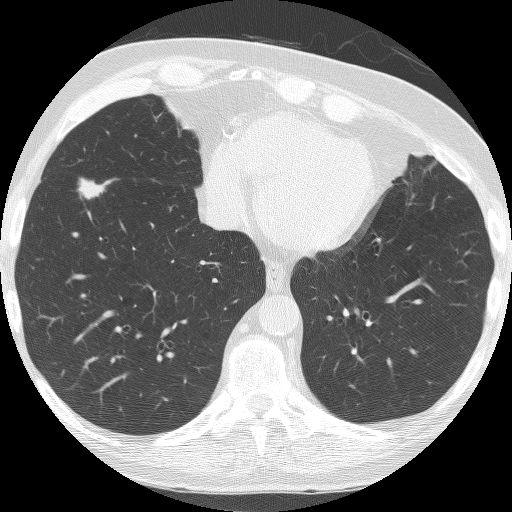
Chest CT (low-dose screening protocol), one axial image; baseline screening round; lung window (W 1500 / L -600 HU); 2.5 mm slice thickness; lung (sharp) reconstruction kernel (BONE); slice 115 of 182 in the series; 512 × 512 image matrix. Male participant, aged 74 years at enrolment.
Lesion marked by an expert reader, bounding box [x1, y1, x2, y2] px = [71, 168, 119, 206]. The screening reader recorded 4 non-calcified nodules or masses ≥4 mm on this exam (right lower lobe, right lower lobe, right lower lobe, right lower lobe); which of them this box marks is not recorded.